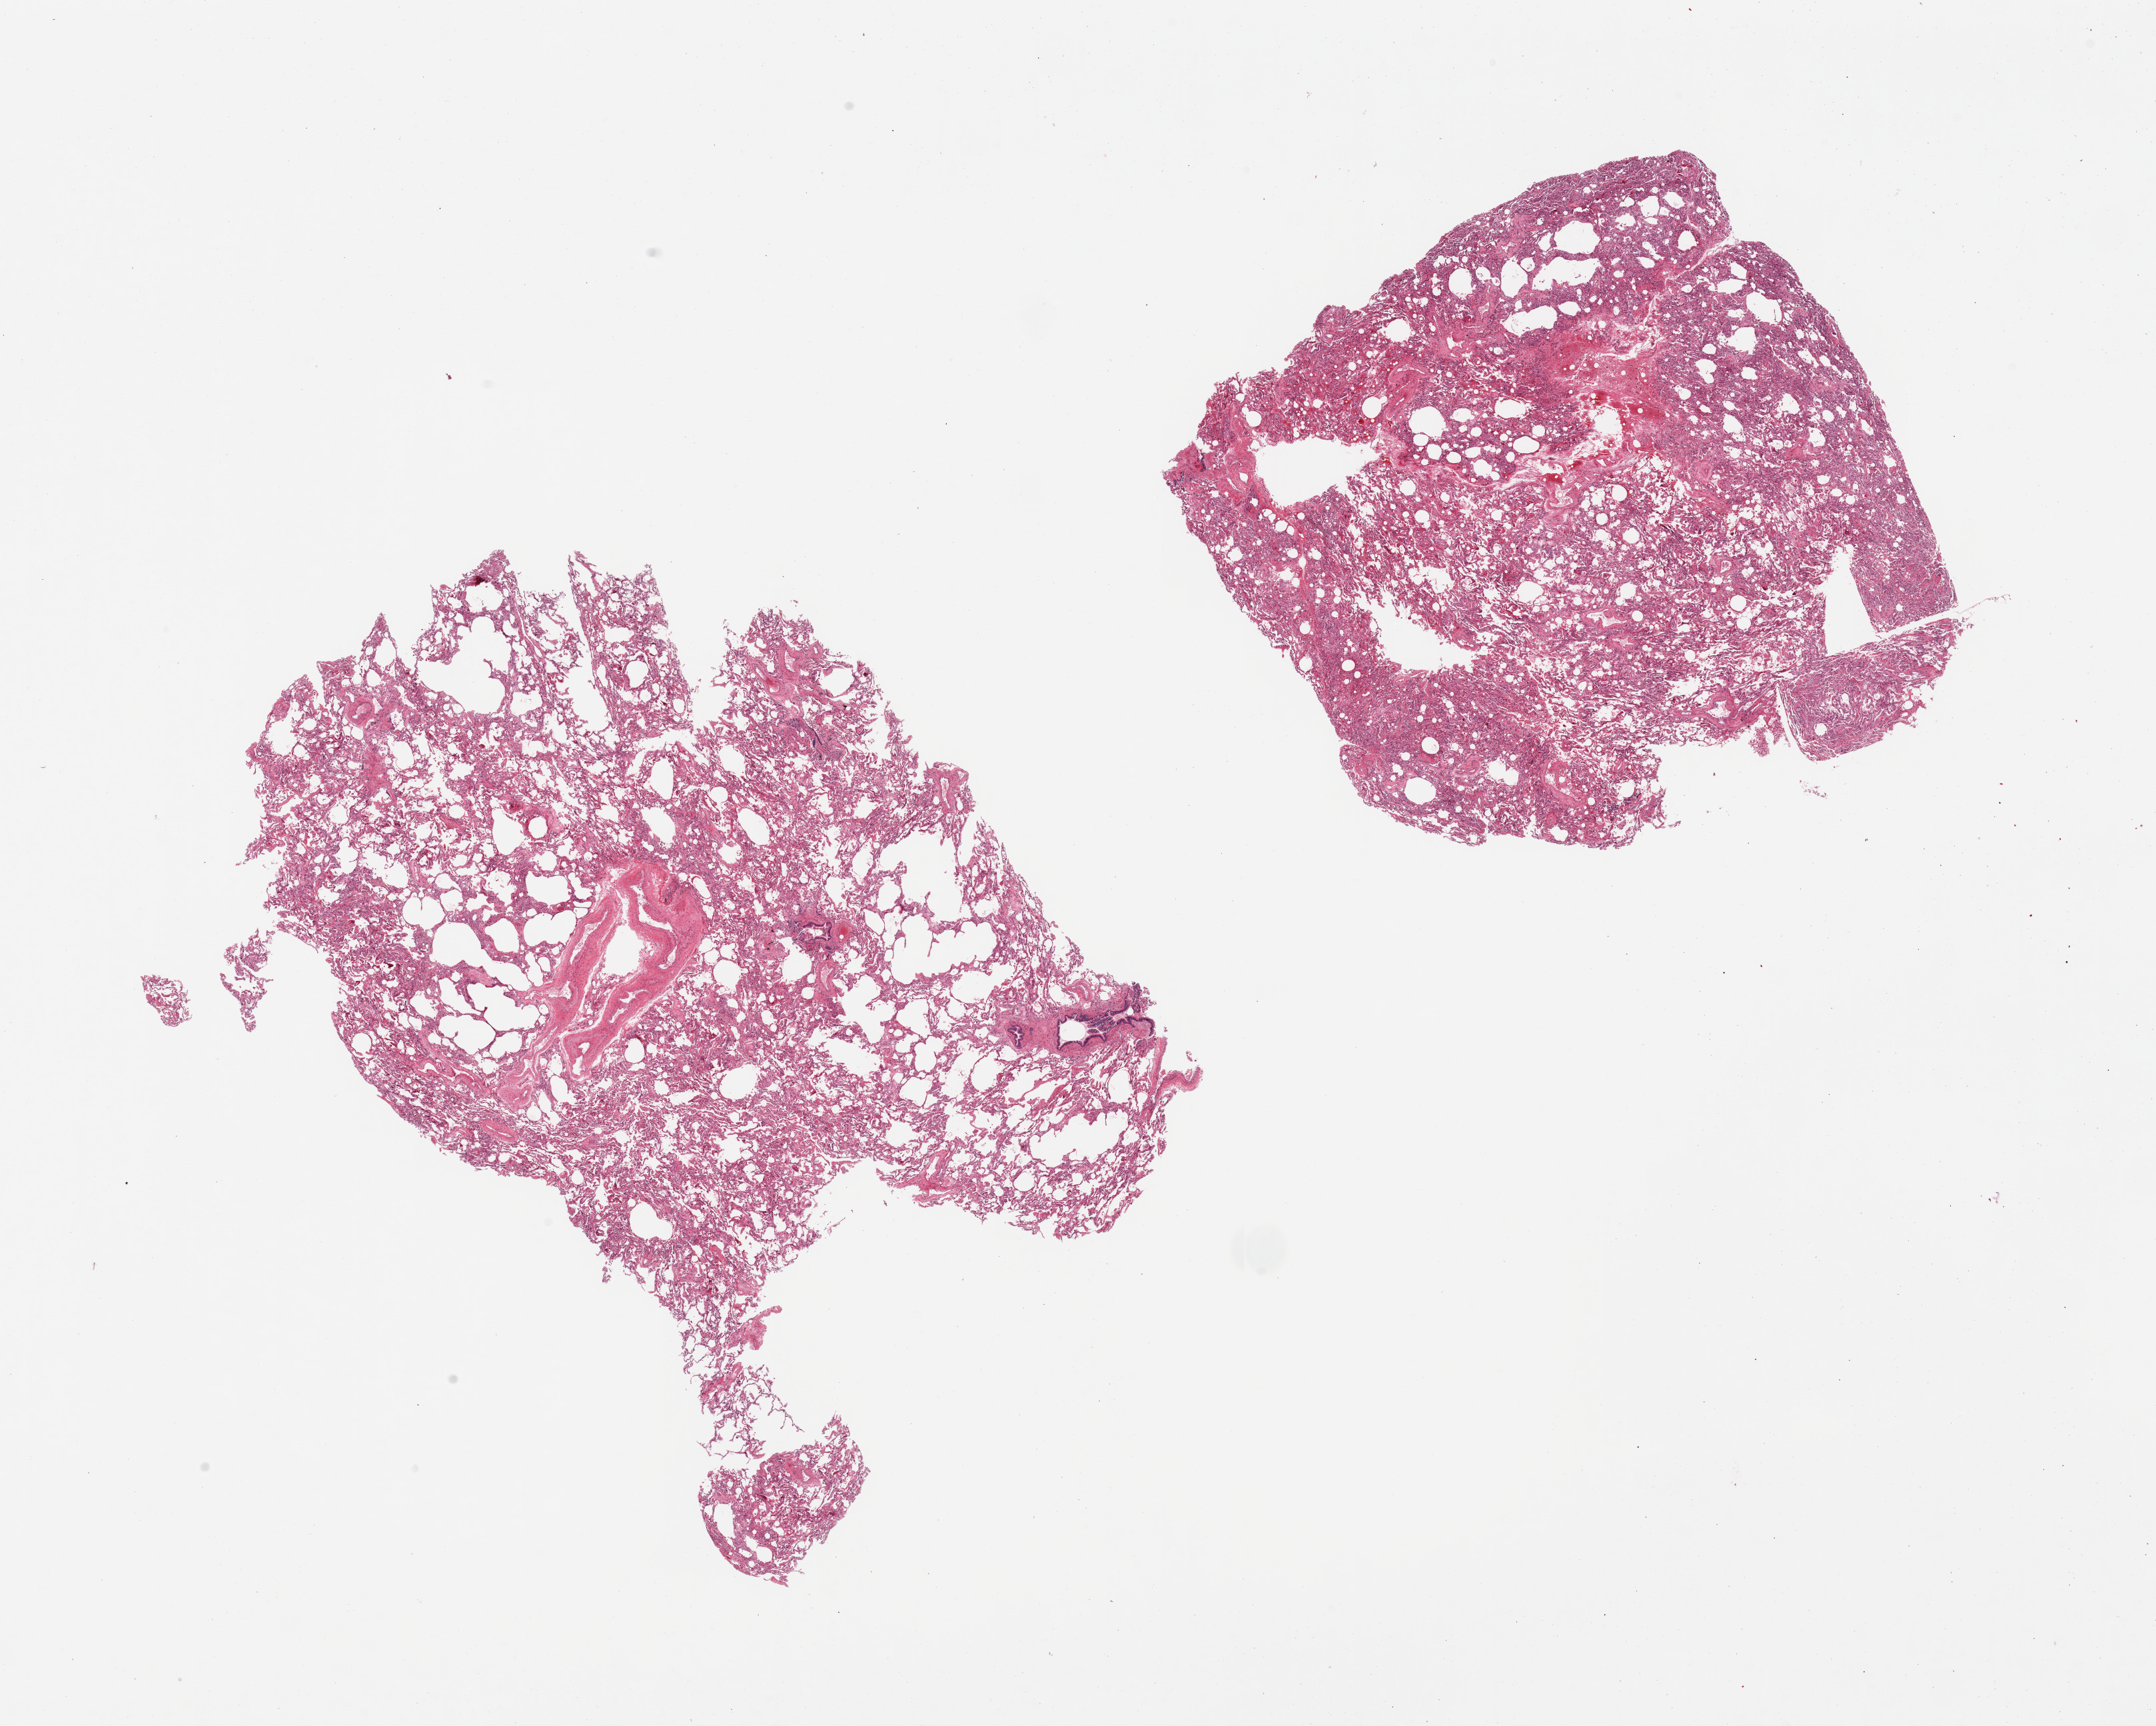
Digitized haematoxylin and eosin-stained section, shown as a low-resolution overview of the whole scanned area (about 25.6 x 20.5 mm, slide scanned at 20x); PAXgene-fixed, paraffin-embedded tissue; target tissue: lung; tissue donor sample.
* review note (as recorded): 2 pieces; patchy emphysema and fibrosis